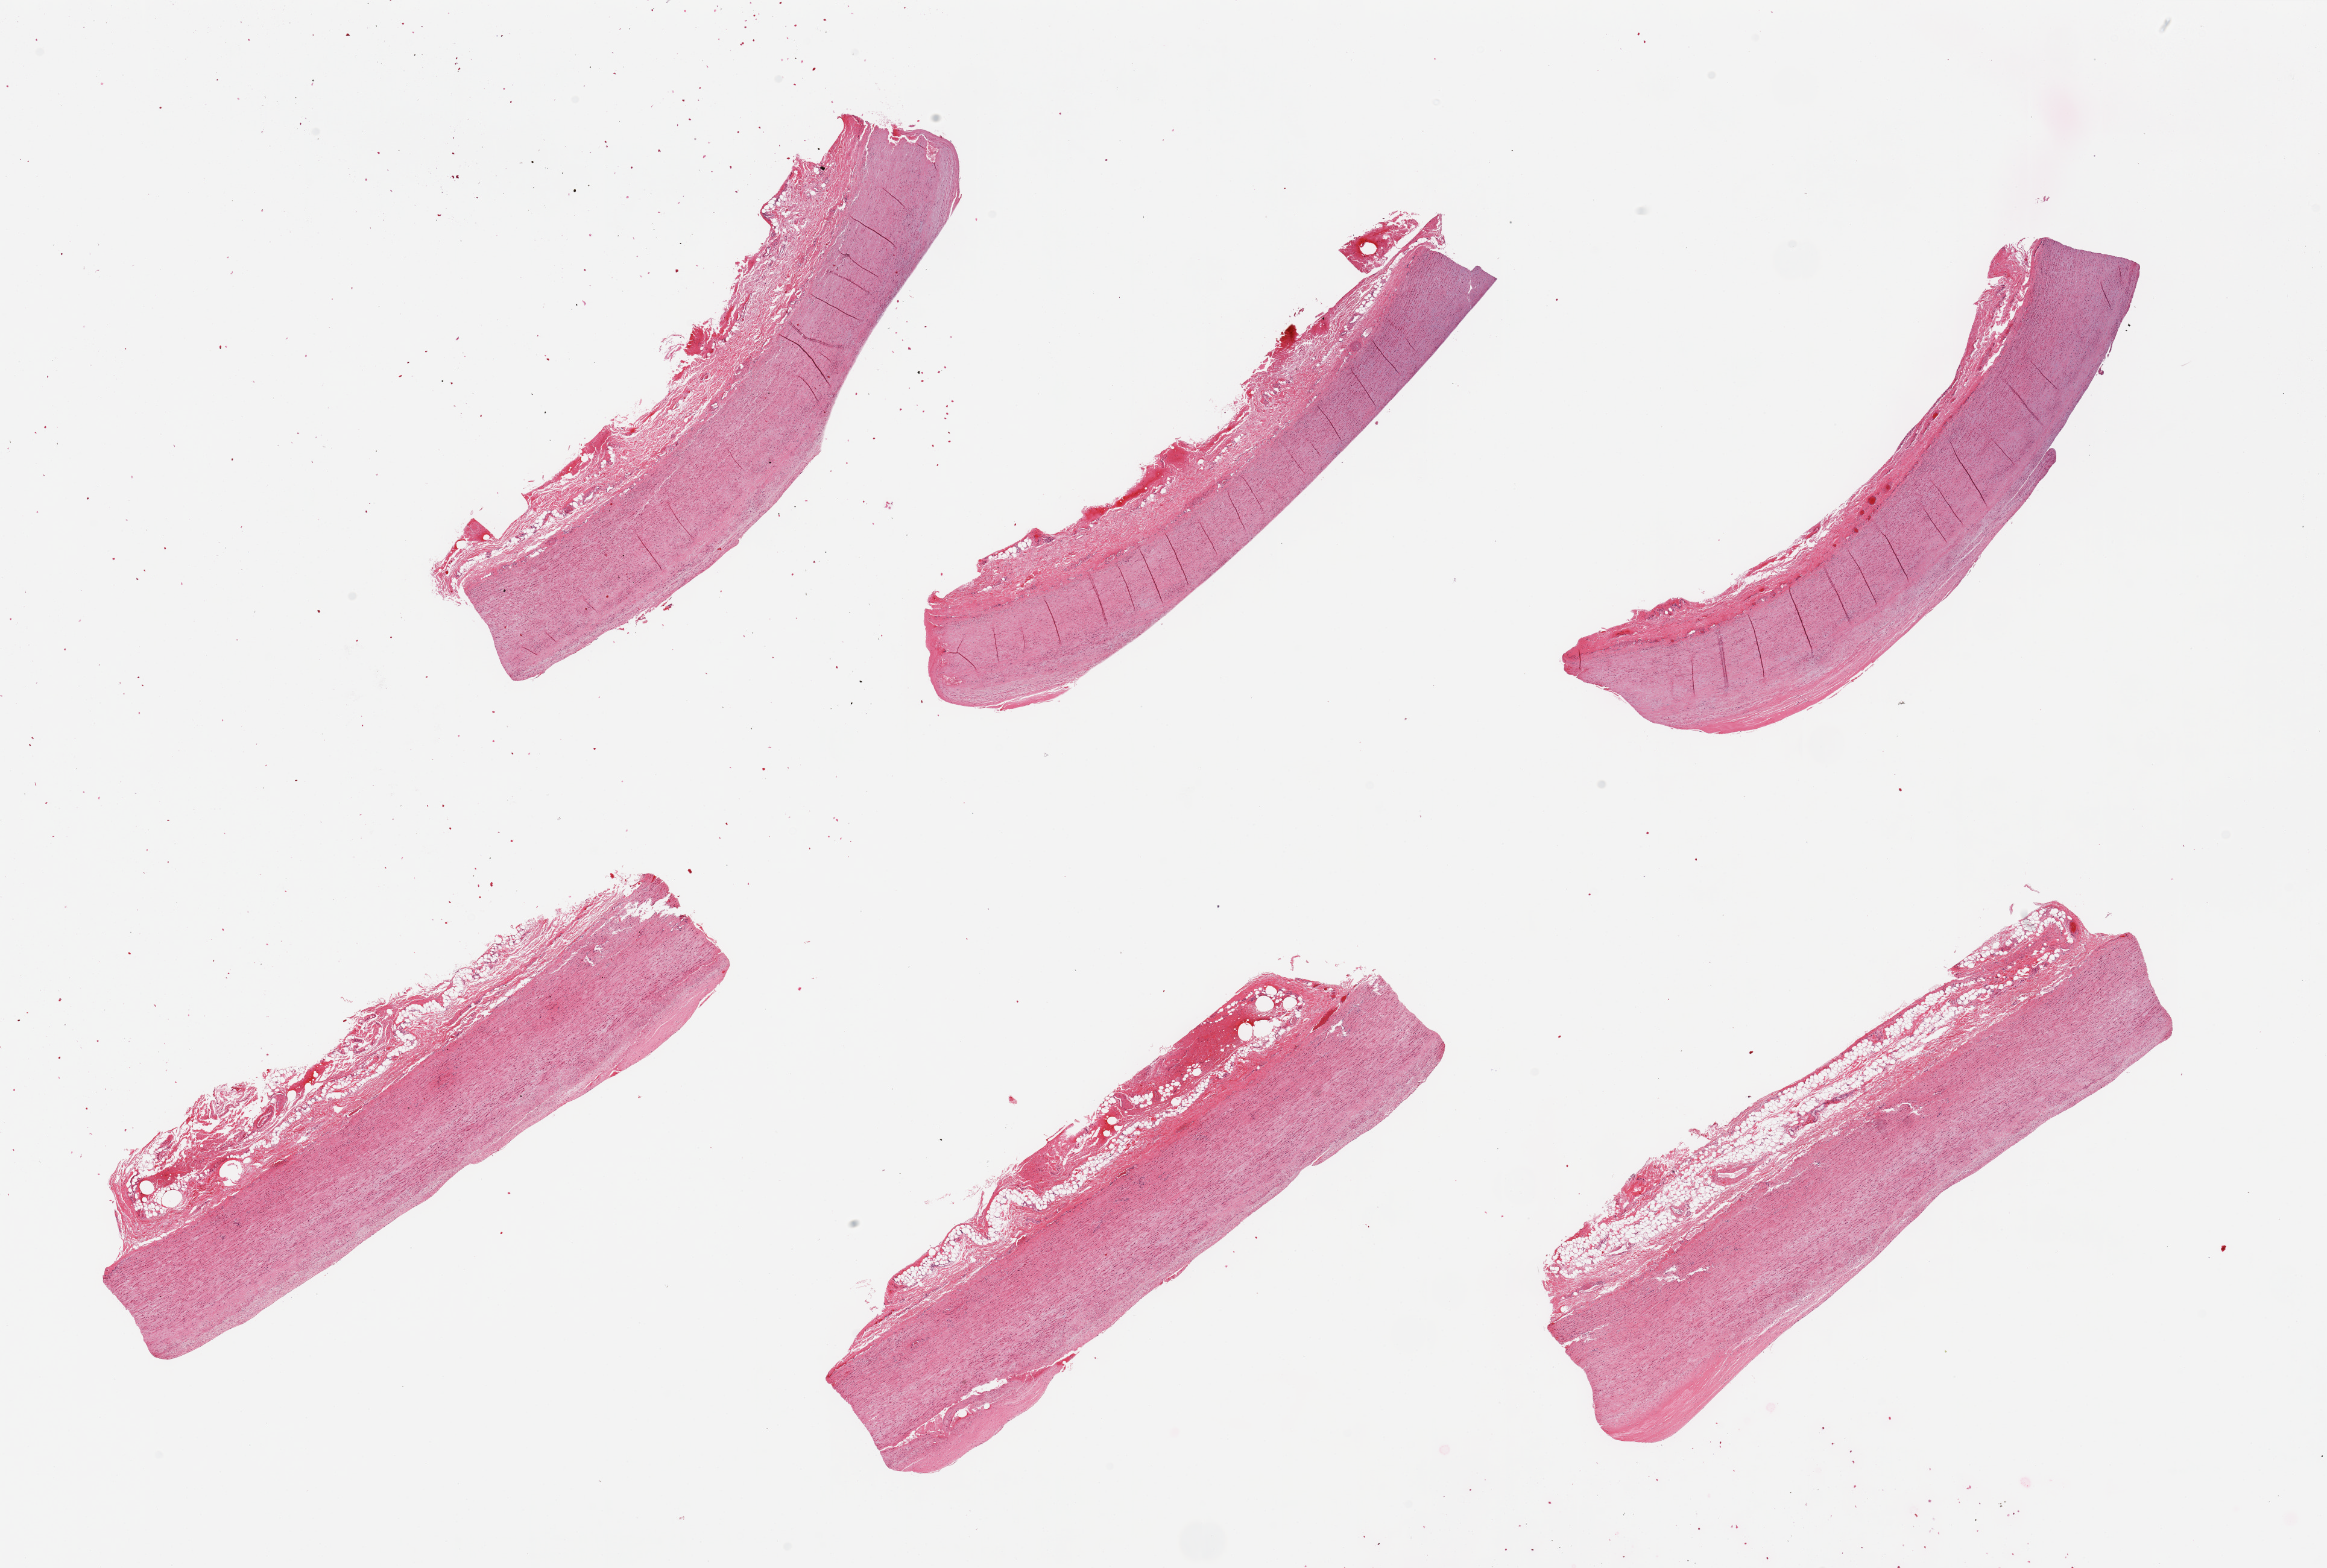
Whole-slide image, hematoxylin and eosin (H&E) stain, shown as a low-resolution overview of the whole scanned area (about 30.5 x 20.6 mm); PAXgene-fixed paraffin-embedded (PFPE) section; target tissue: aorta; donor tissue sample.
Pathologist's review note for this sample: 6 pieces; atherosclerosis, thick adventitia.